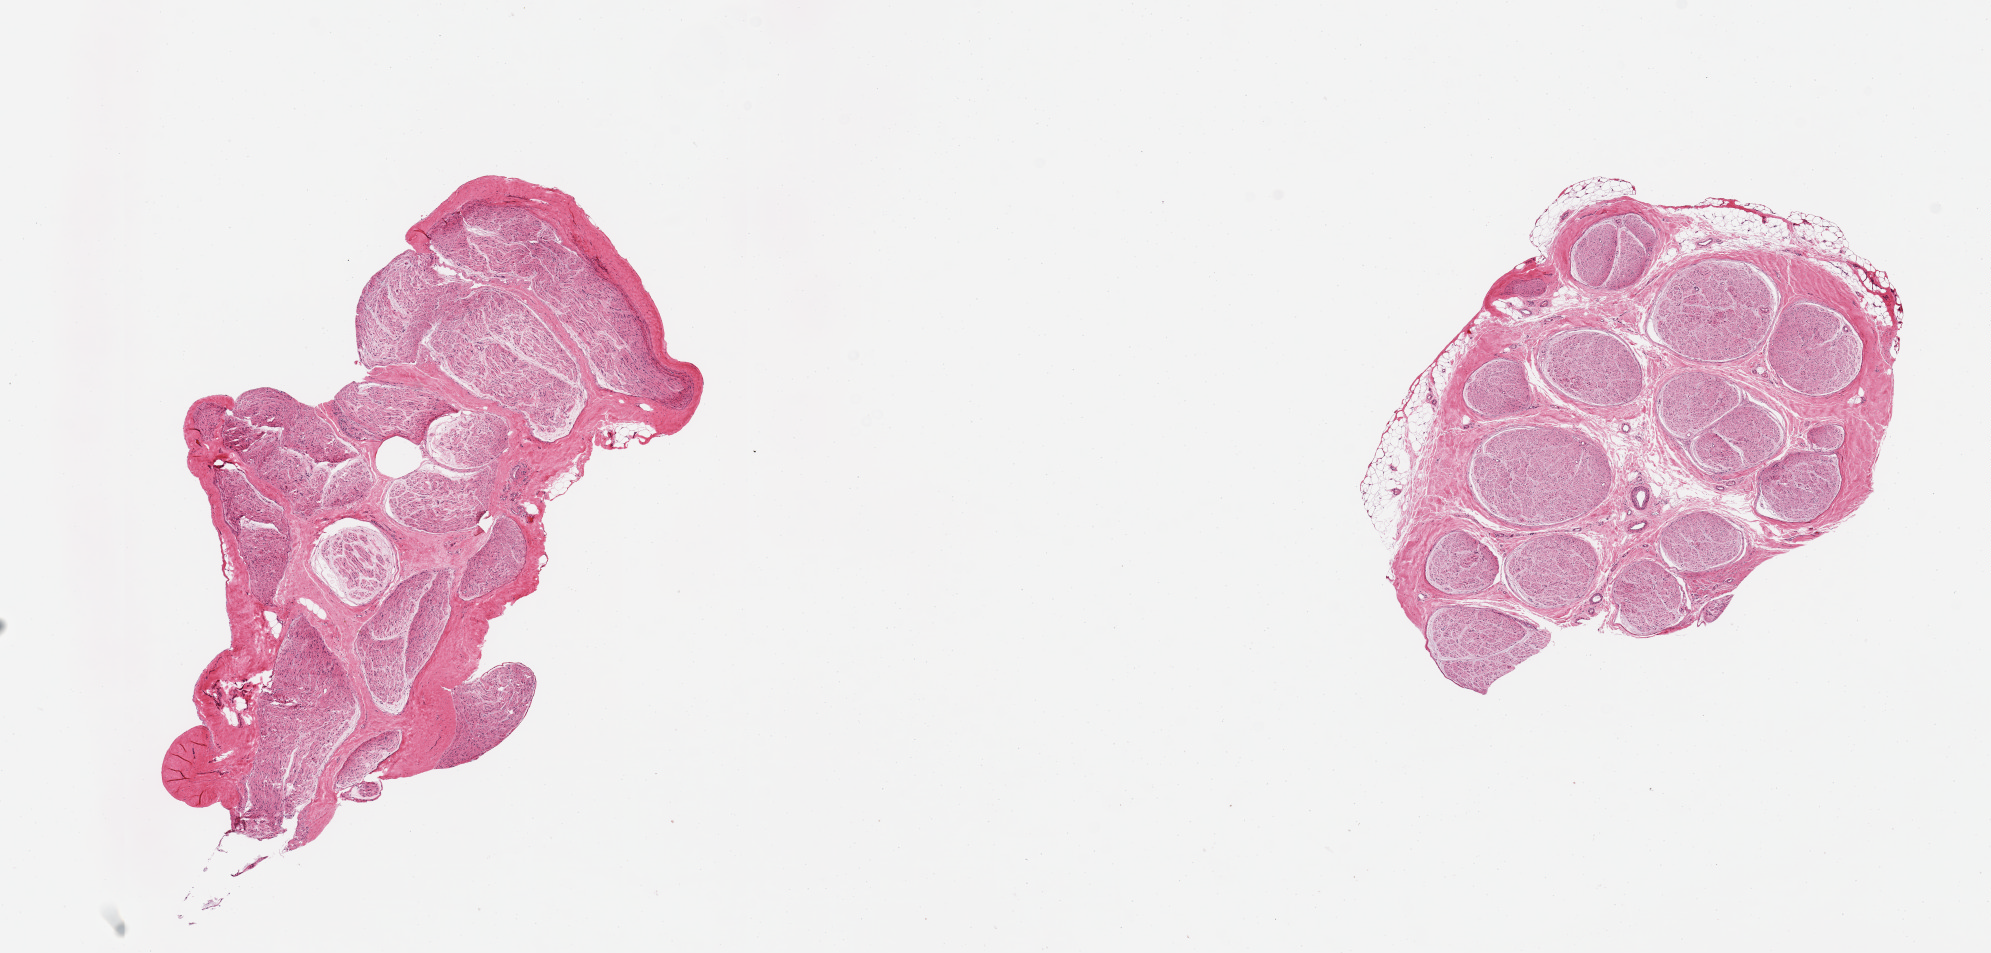
H&E whole-slide image — a low-resolution overview of the entire scanned area, about 15.8 x 7.5 mm (slide scanned at 20x); PAXgene-fixed paraffin-embedded (PFPE) section; sampled site (target tissue): tibial nerve; donor tissue sample. Male donor.
Reviewer comment on this tissue sample: 2 pieces, peripheral nerve, trace adherent fat.